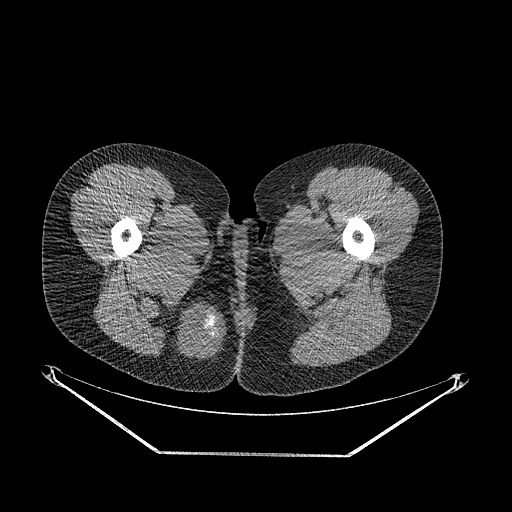
CT of an extremity soft-tissue mass (from a PET/CT study), one axial slice. Slice 26 of 267 in the series (ordered by position). 120 kVp. Soft-tissue window (W 400 / L 40 HU). 3.75 mm slice thickness. 512 × 512 image matrix, field of view 500 × 500 mm. Female patient. From the clinical record (not read from this slice): histological type: epithelioid sarcoma; grade: intermediate; site of the primary tumour: right buttock.
Annotated regions visible in this slice (expert contour drawn on MRI and transferred to this co-registered scan by the dataset authors):
- gross tumour volume including surrounding oedema: bounding box <171,301,225,359> (left, top, right, bottom; pixels)
- gross tumour volume (mass): <176,304,225,357>